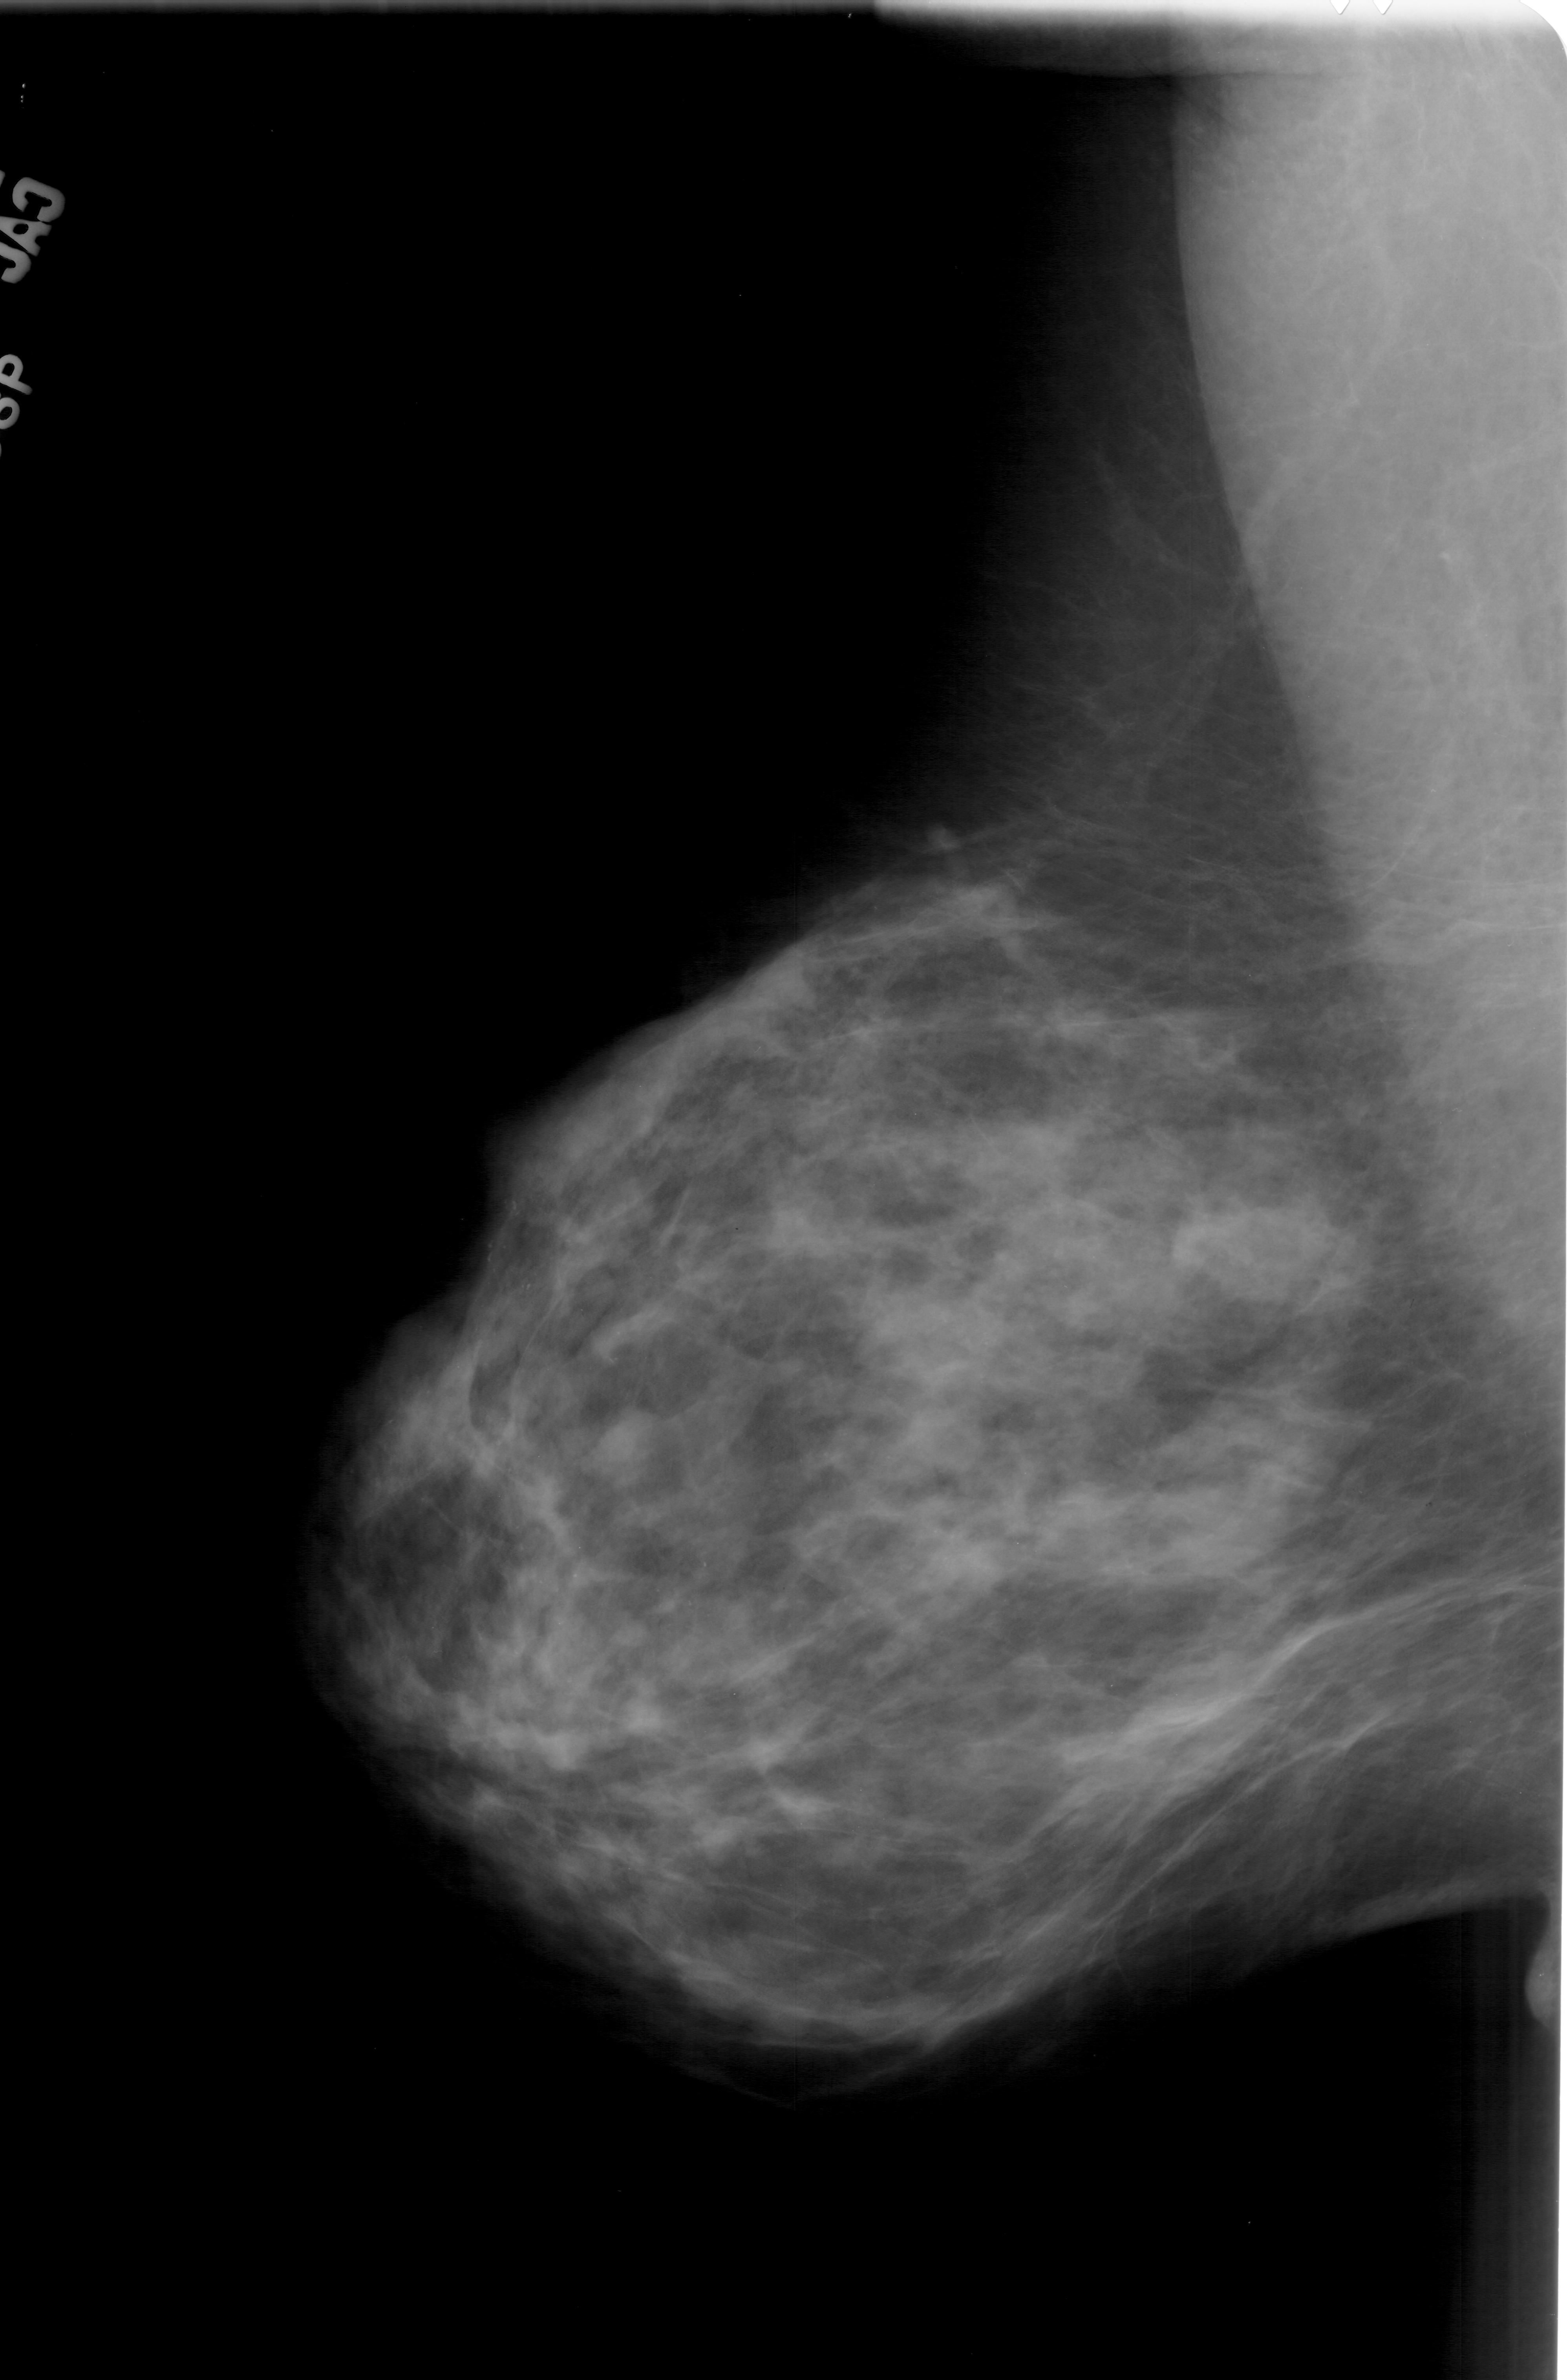
Digitized screen-film mammogram, left breast, MLO view.
Radiologist-marked abnormalities on this image: calcifications, morphology pleomorphic, distribution segmental; BI-RADS assessment category 4; subtlety rating 3 on a 1 (subtle) to 5 (obvious) scale; pathology result (as recorded, not read from the image): malignant.